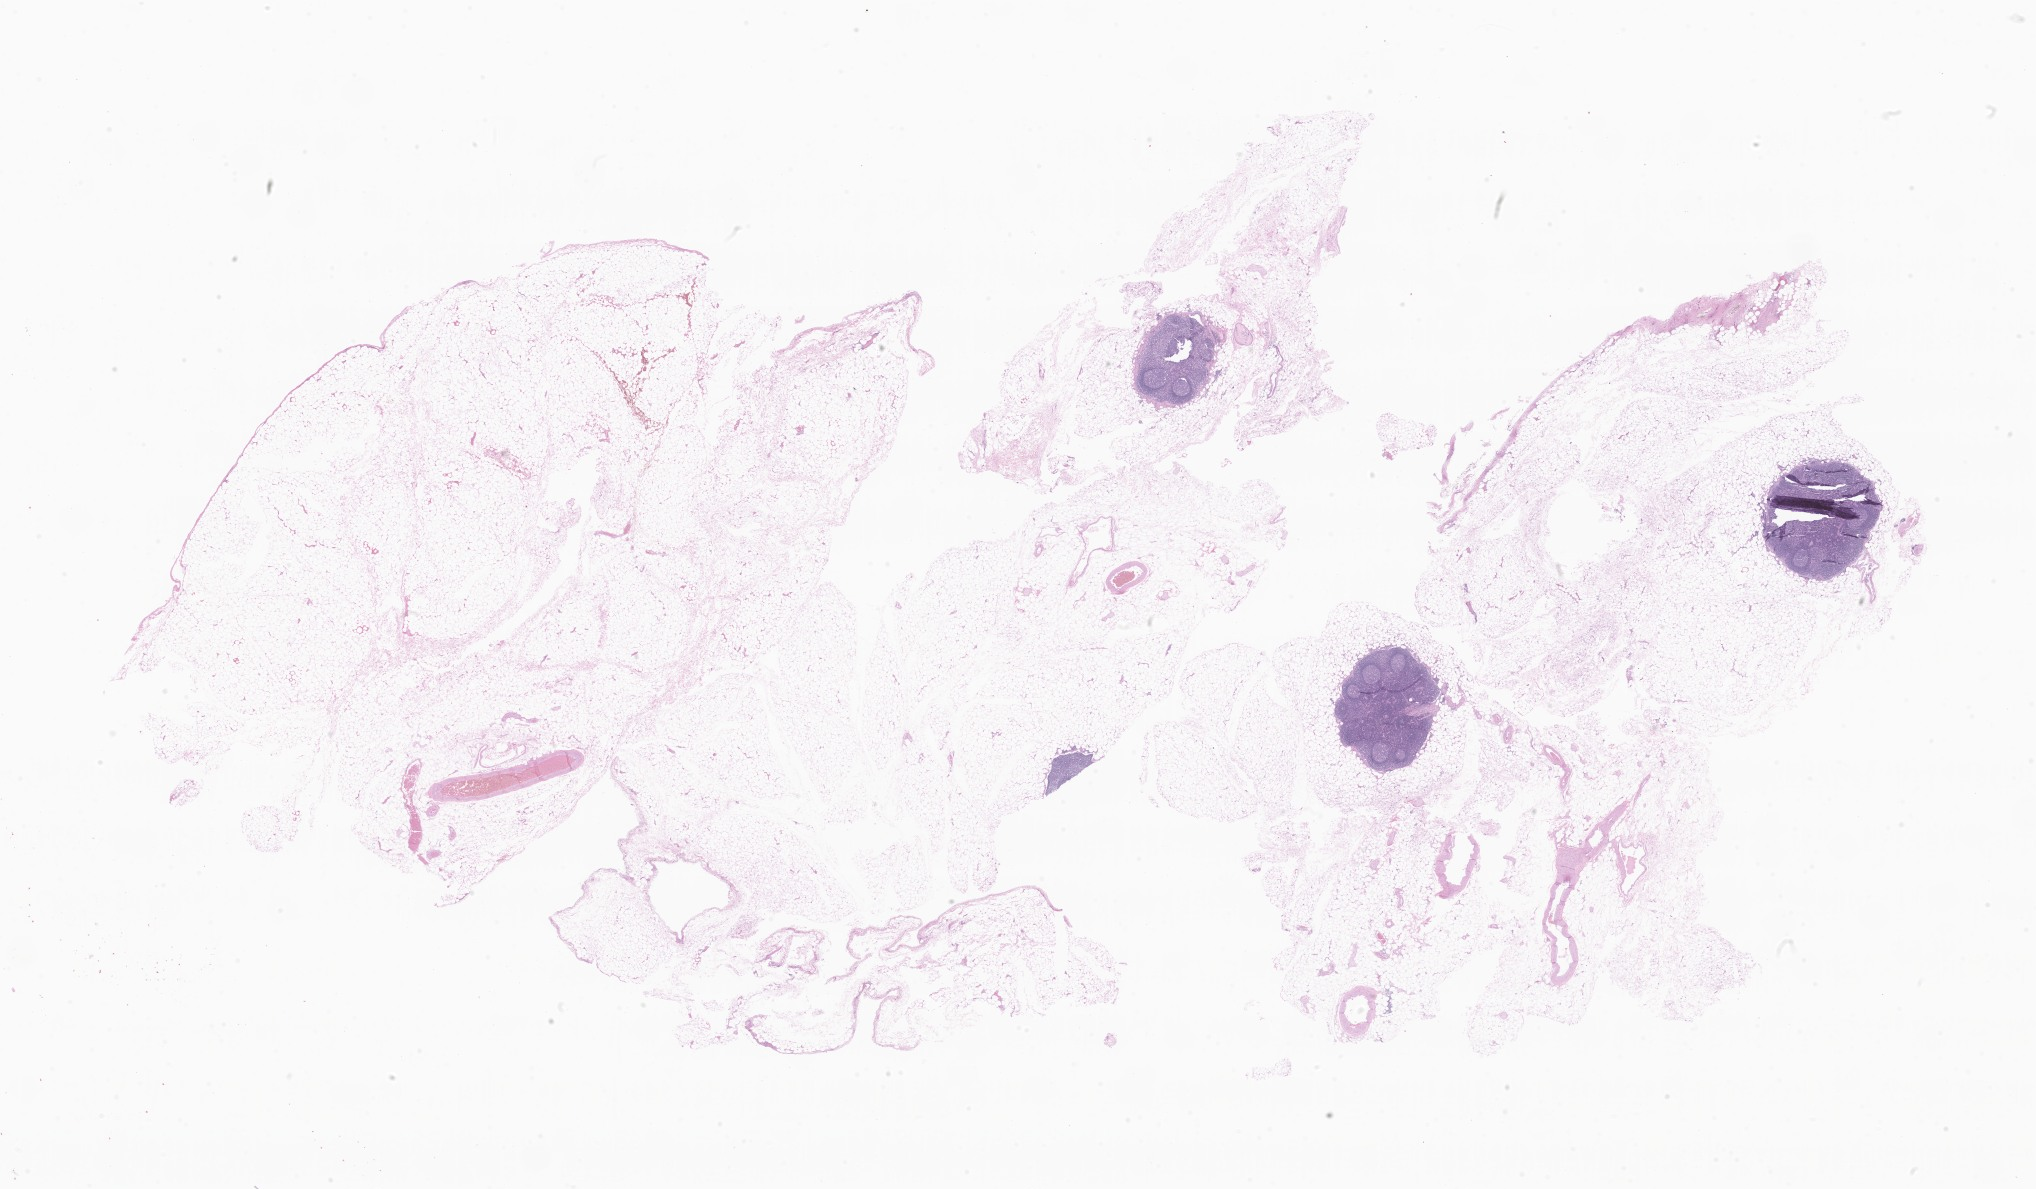
Digitized H&E-stained section, a low-resolution overview of the entire scanned area, about 34.3 x 20.1 mm, formalin-fixed, paraffin-embedded (FFPE) tissue, specimen: non-tumor (normal tissue) sample from a patient with adenocarcinoma, NOS, site: rectum. Patient: male, age at initial diagnosis 65 years. Pathologist review of this section (percent, as recorded): tumor cells 0%, tumor nuclei 0%, stromal cells 100%, necrosis 0%, normal cells 0%. Inflammatory infiltration, as recorded: lymphocyte infiltration 70%, monocyte infiltration 5%, neutrophil infiltration 8%.
This section: non-tumor tissue sample; the patient's diagnosis is given above. Section: top of the tissue portion.